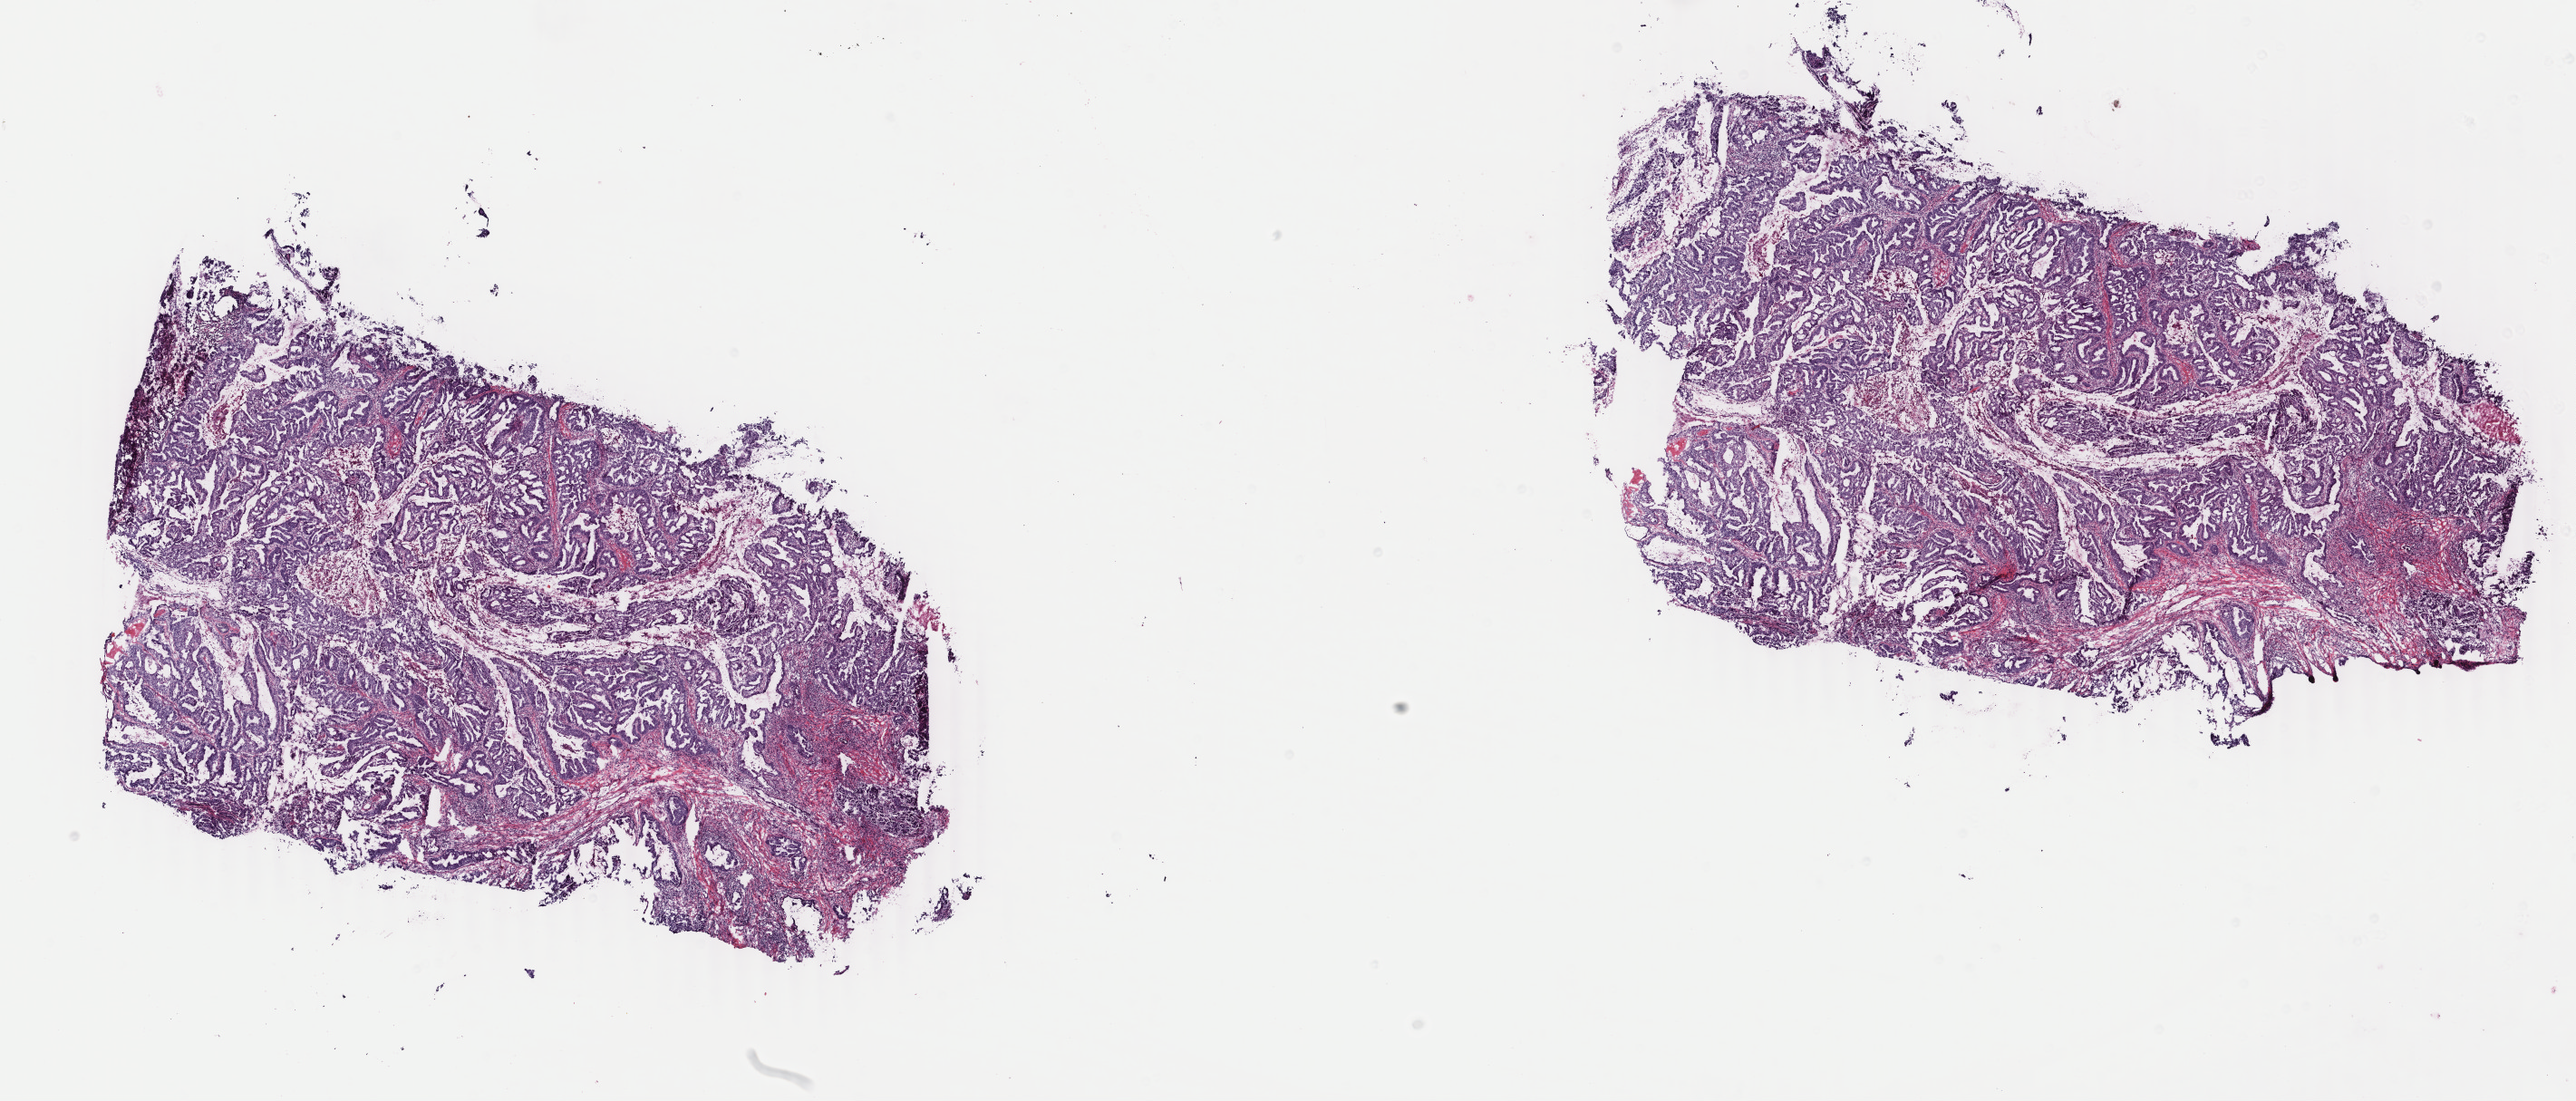
Whole-slide histology image, H&E-stained — a low-resolution overview of the entire scanned area, about 22.6 x 9.7 mm; frozen section; sample: primary tumour, uterus. Female, age 88 years at initial diagnosis. Histologic grade: G1 (well differentiated). Pathologist review of this section (percent, as recorded): tumour cells 70%, tumour nuclei 80%, normal cells 20%, stromal cells 0%, necrosis 10%. Infiltration values recorded for this section: lymphocyte infiltration 20%, monocyte infiltration 0%, neutrophil infiltration 20%.
FIGO stage: II. Diagnosis: Endometrioid adenocarcinoma, NOS (endometrium).